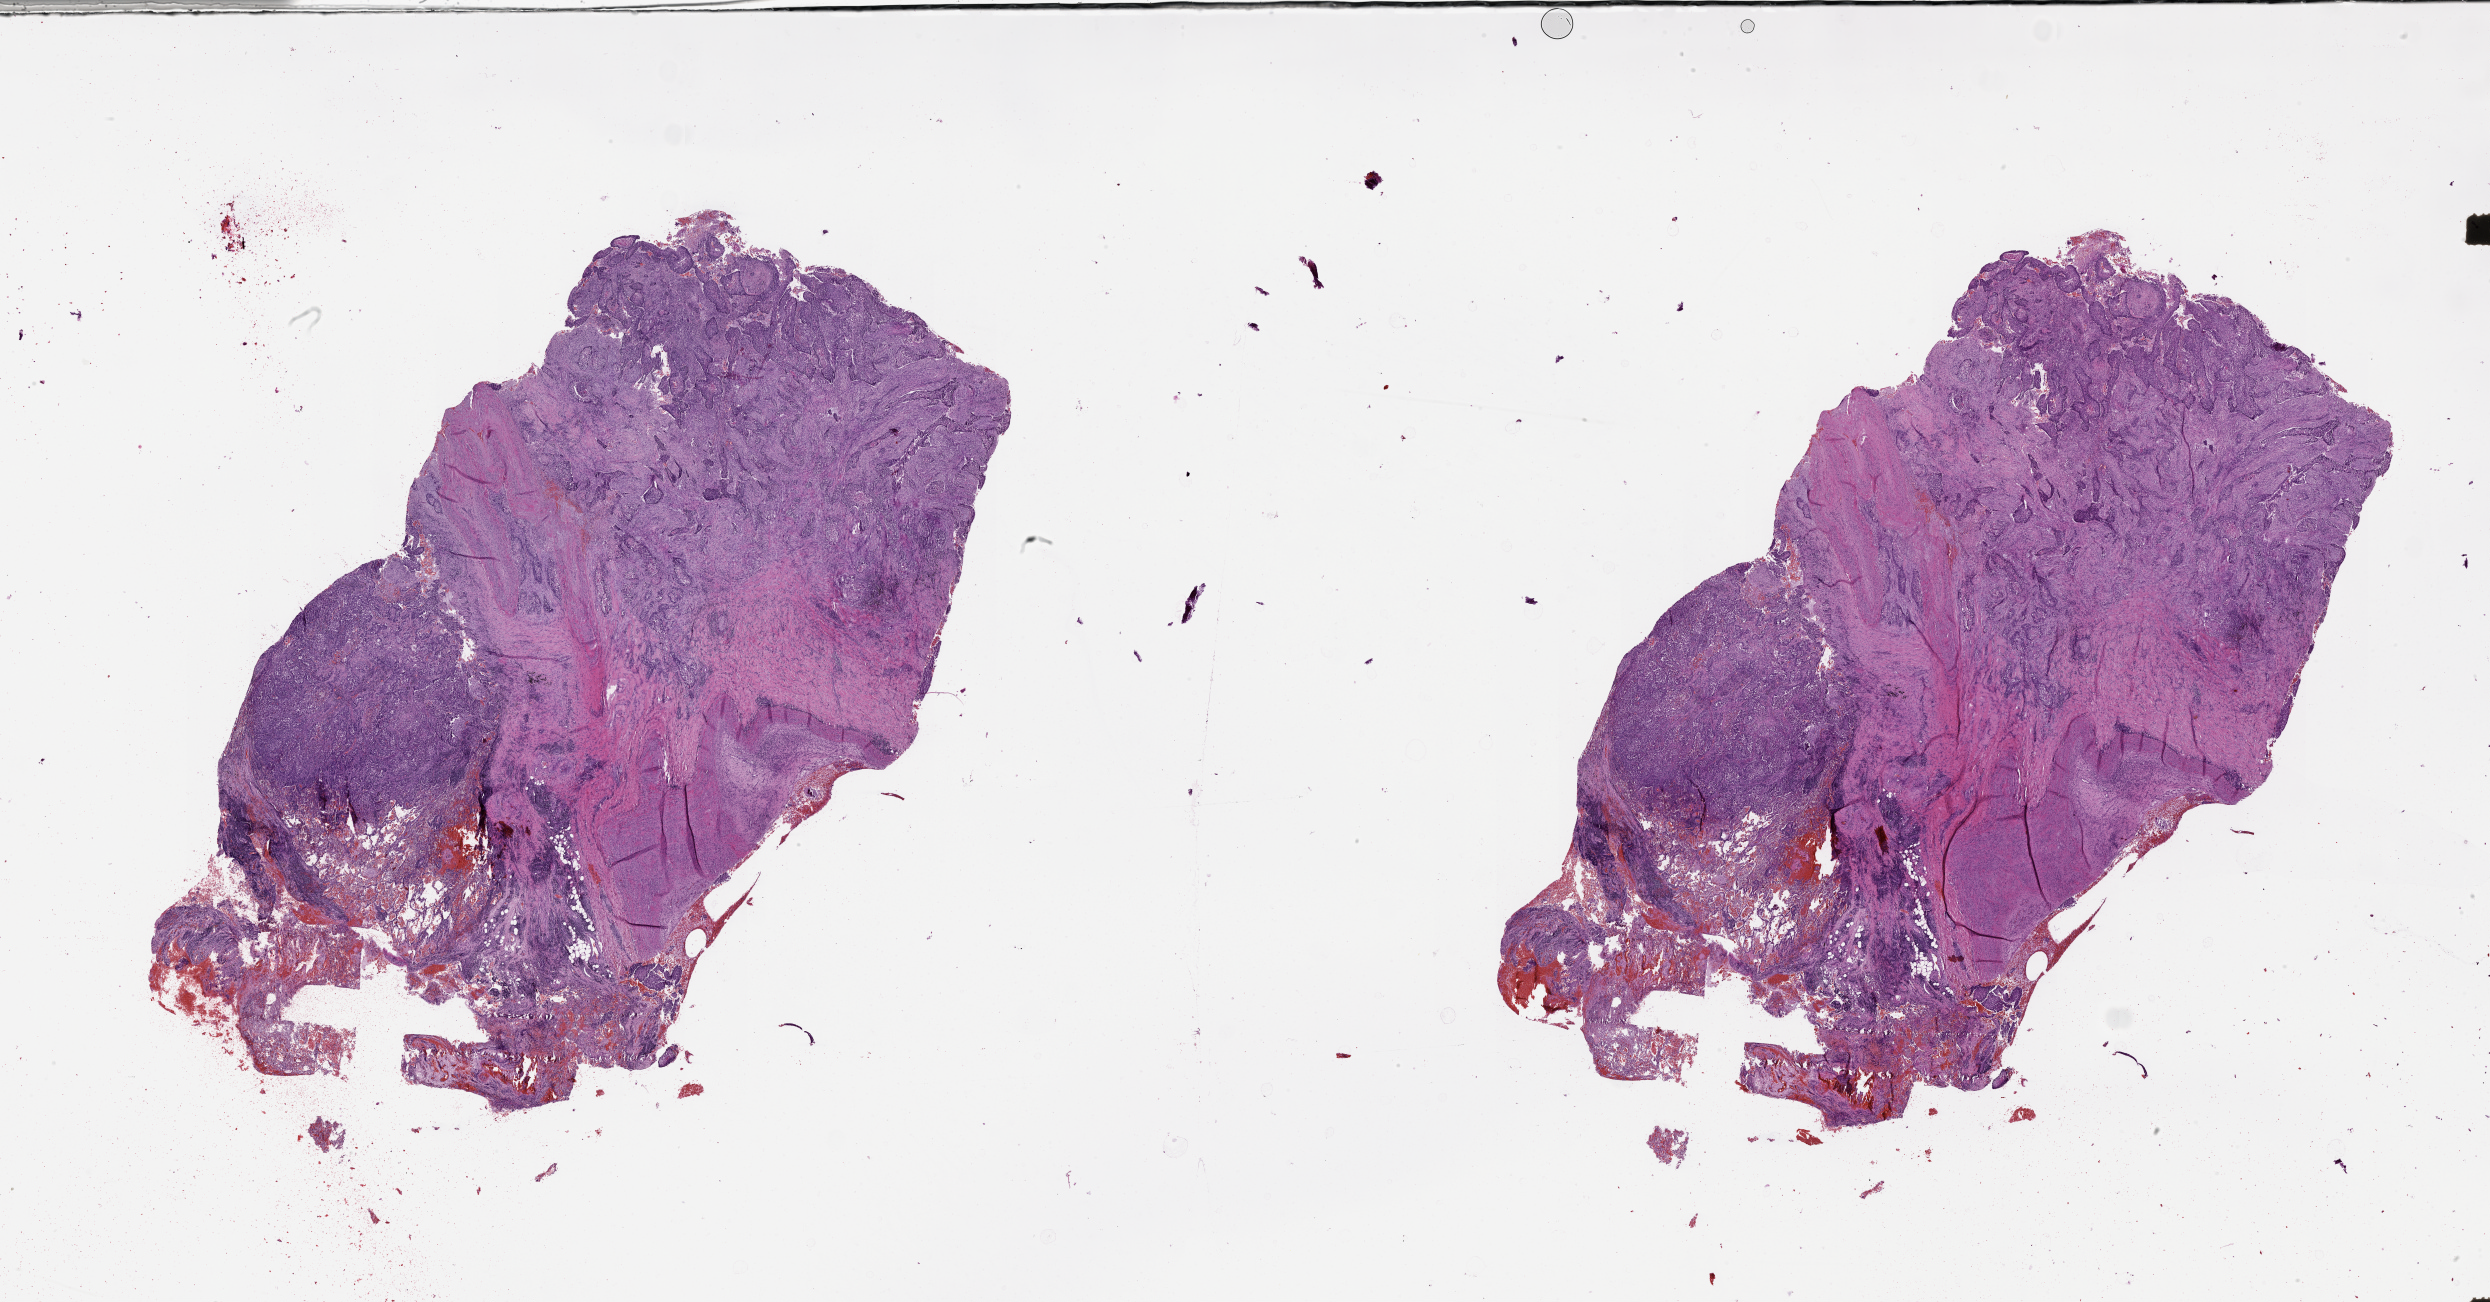
Hematoxylin and eosin (H&E) stained whole-slide image — whole scanned area (about 40.1 x 21.0 mm, from a 20x scan) shown as a low-resolution overview; lung, tumour tissue. 49-year-old male patient.
Patient diagnosis (cohort enrolment): squamous cell carcinoma (lung).